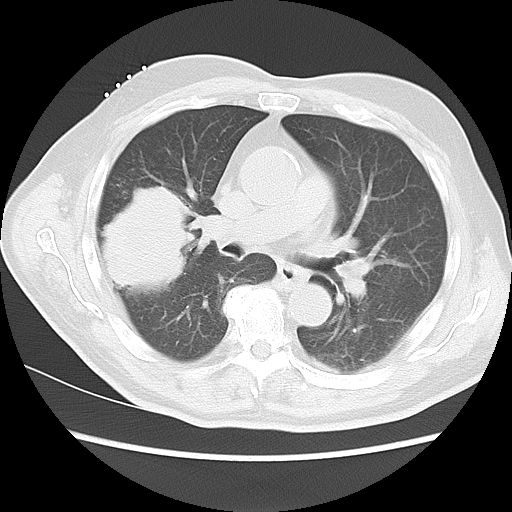
Chest CT, one axial slice; slice 6 of 15 in the series (ordered by position); reconstruction kernel LUNG; lung window (W 1500 / L -600 HU); 5 mm slice thickness; 512 × 512 image matrix, field of view 350 × 350 mm. Patient: male, 68 years. From the clinical record (not read from this slice): clinical TNM (as recorded): T4 N3 M0.
Outlined on this slice (bounding box drawn by a radiologist):
- lung tumour (recorded histology: squamous cell carcinoma): bounding box (x1, y1, x2, y2) in pixels: (99, 170, 199, 289)